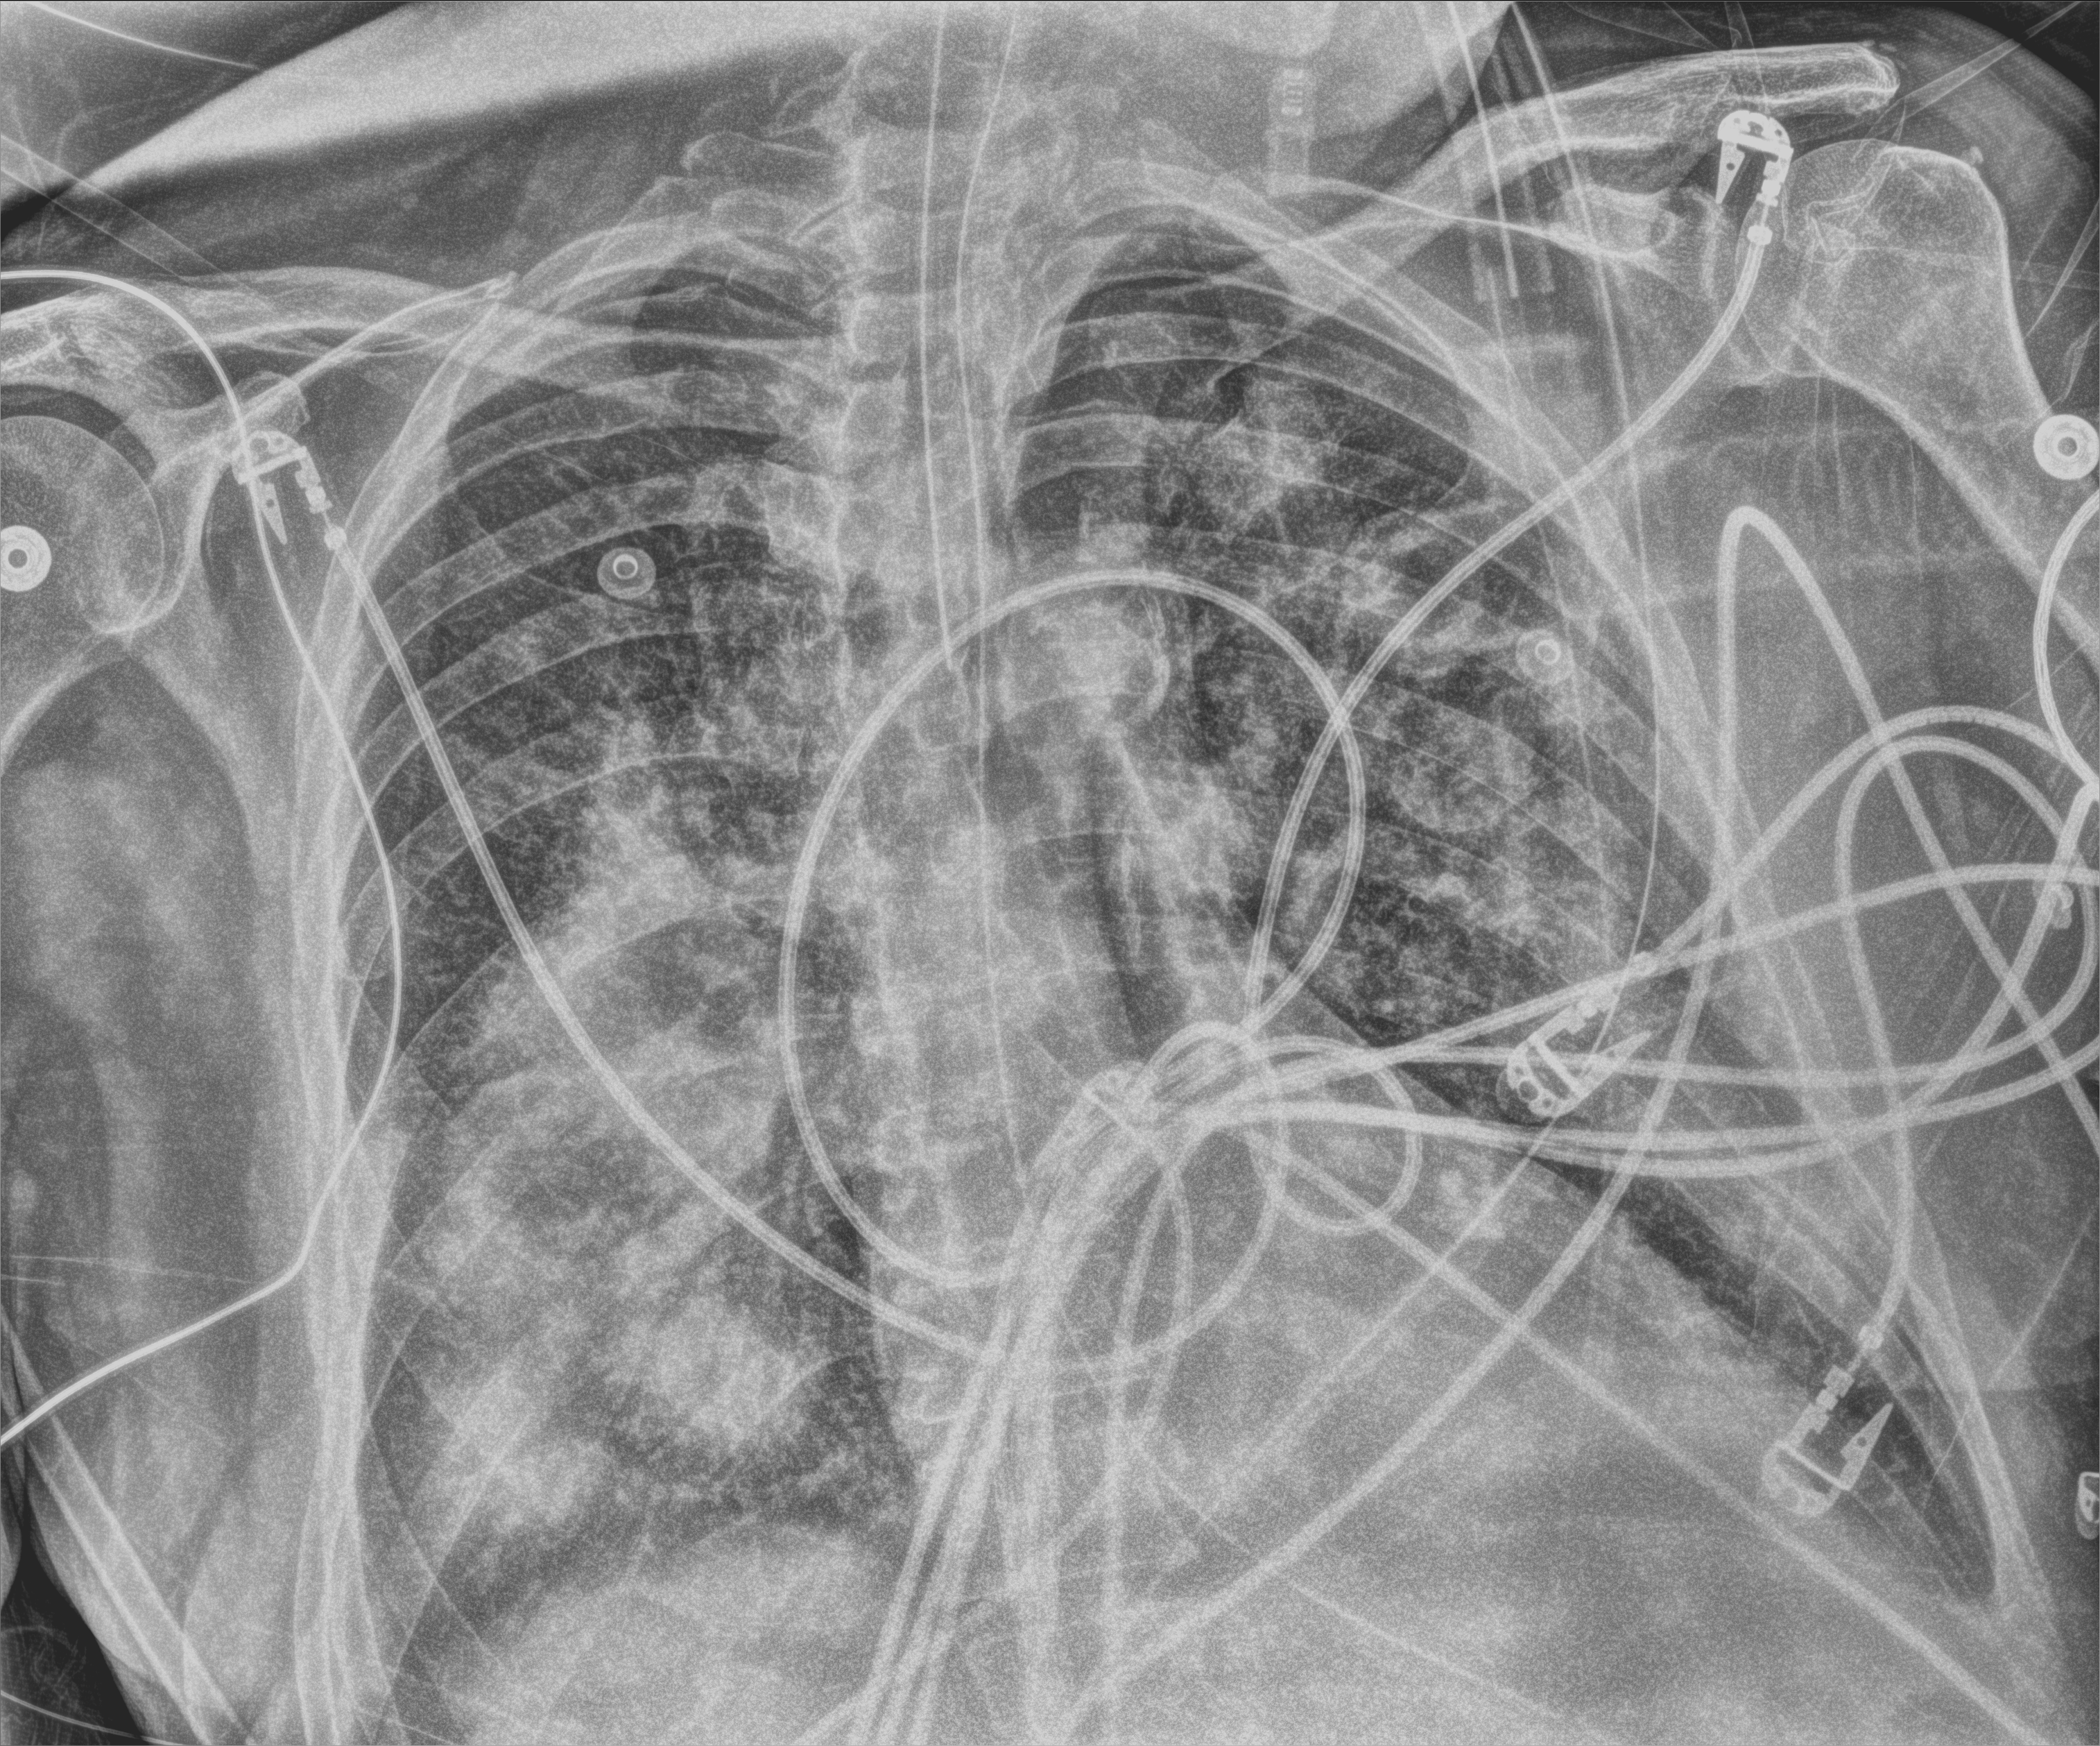
Bedside chest radiograph (computed radiography), anteroposterior (AP) projection. Patient hospitalised with COVID-19; male, aged 60–74 years.
From the hospital-stay record, not from the radiograph (when in the stay this image was taken is not recorded): admitted to intensive care during this hospital stay: yes; mechanically ventilated during this hospital stay: yes.